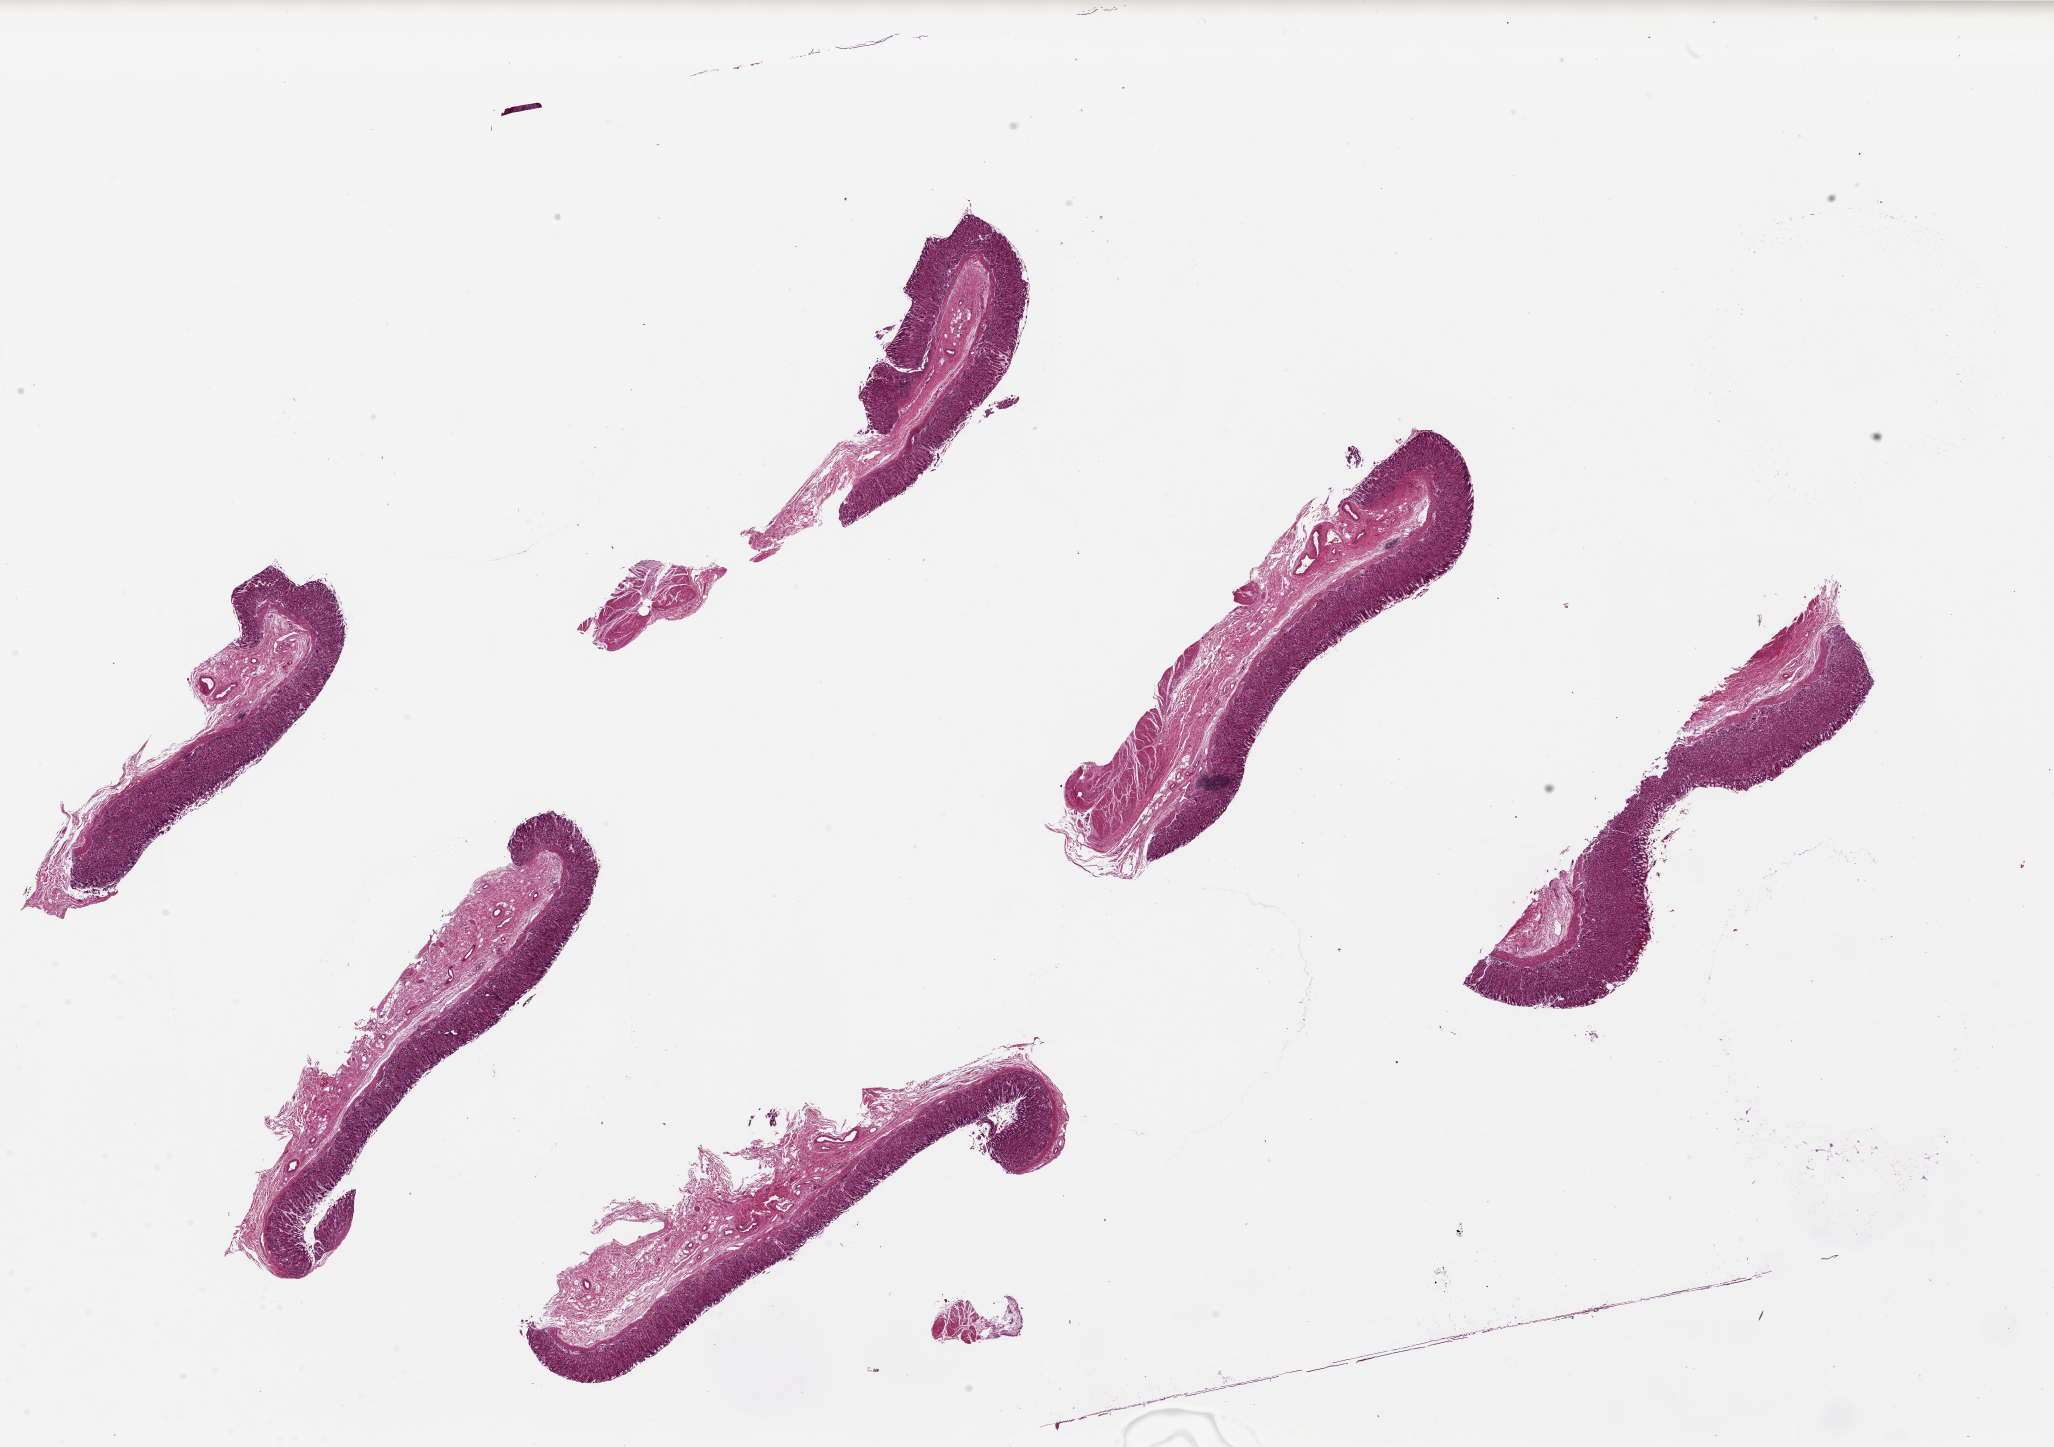
Whole-slide image, hematoxylin and eosin (H&E) stain — whole scanned area (about 32.5 x 22.9 mm, from a 20x scan) shown as a low-resolution overview. PAXgene-fixed, paraffin-embedded tissue. Sampled site (target tissue): stomach. Tissue donor sample. Donor sex: female.
Reviewer comment on this tissue sample: 6 pieces, up to 9x2mm; oxyntic mucosa with sloughed superficial layer; No muscularis propria present.